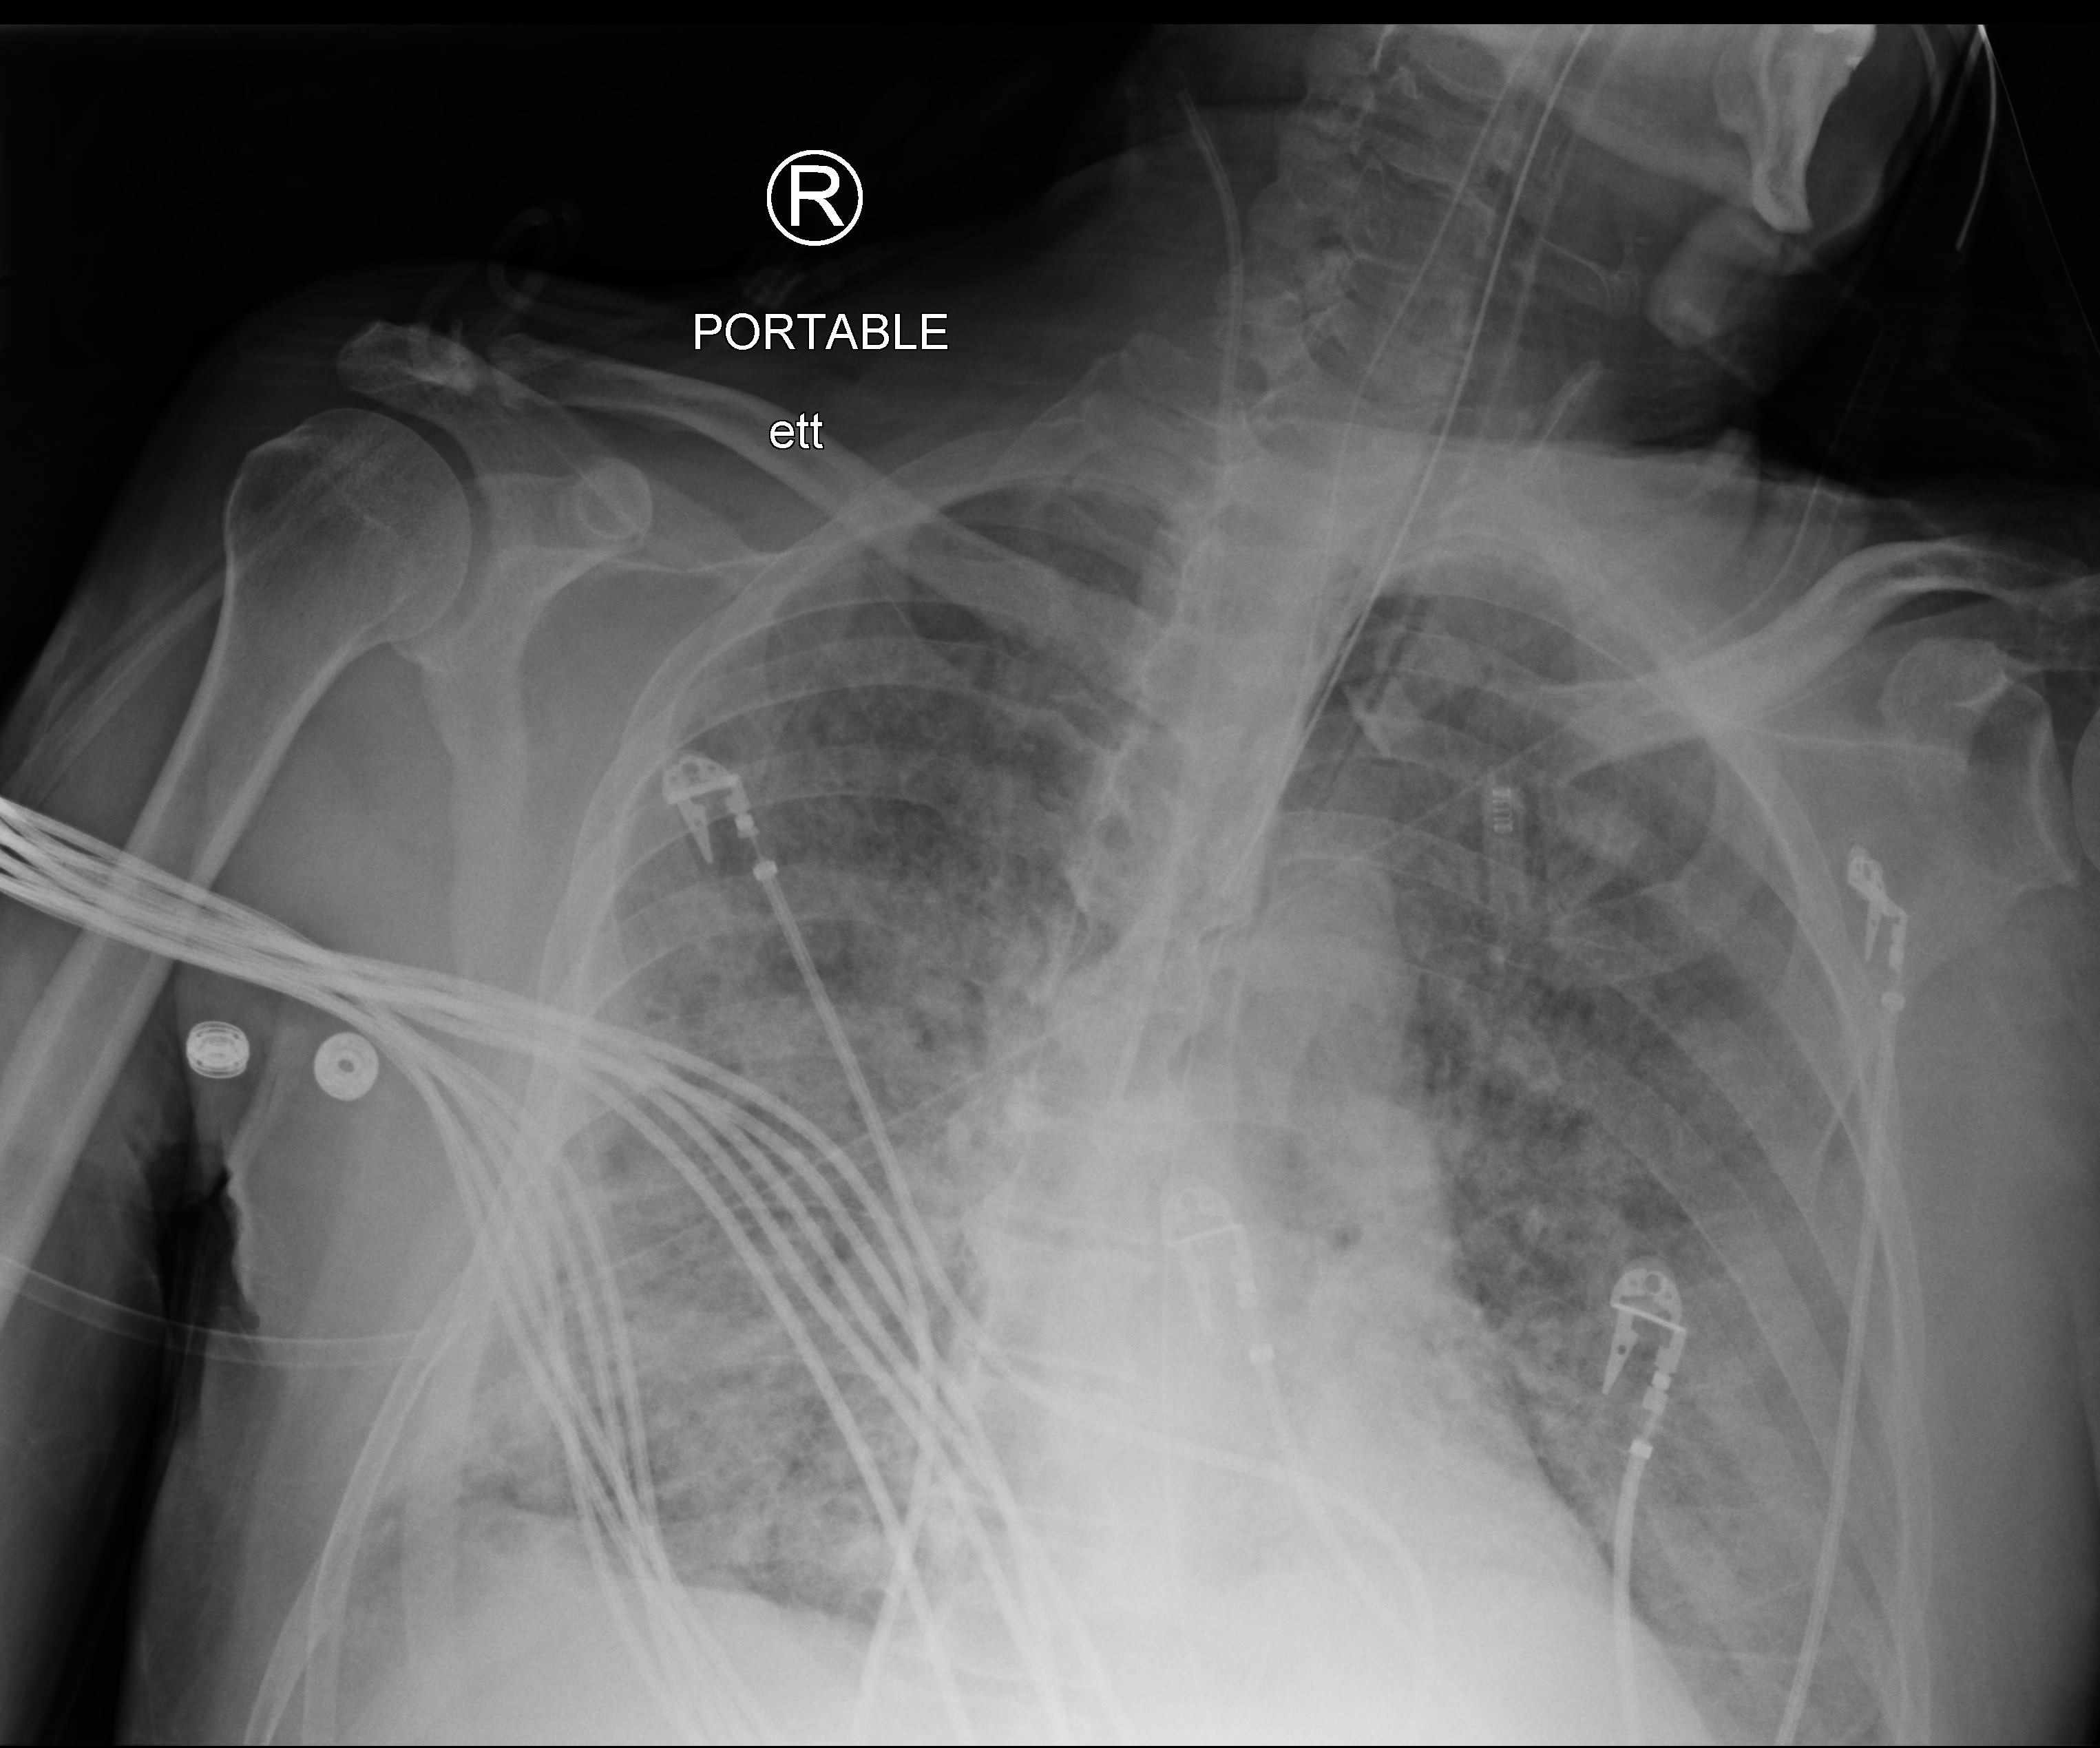
Chest X-ray (portable). Male patient hospitalised with COVID-19, age 60–74 years.
Admission-level facts for this patient (not findings on this image; timing relative to this image not recorded): admitted to intensive care during this hospital stay: yes; mechanically ventilated during this hospital stay: yes; smoking status (admission record): never.